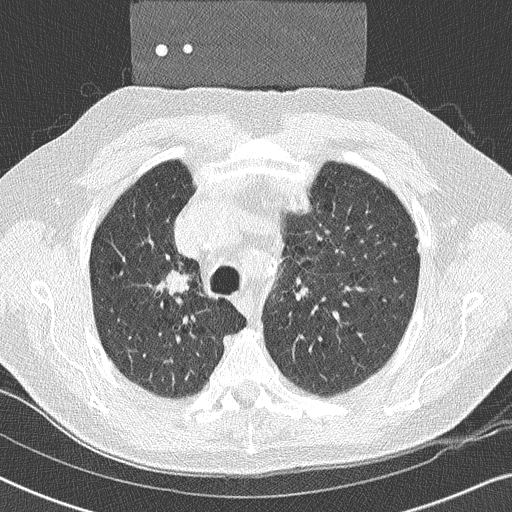
Low-dose screening chest CT, one axial slice; slice 180 of 252 in the series (ordered by position); reconstruction kernel B50f; lung window (W 1500 / L -600 HU); 2 mm slice thickness; 512 × 512 image matrix, field of view 330 × 330 mm.
Outlined on this slice (manually delineated by an expert):
- lesion 1 (tumor, upper lobe of right lung): bounding box [x1, y1, x2, y2] px = [166, 271, 187, 293]